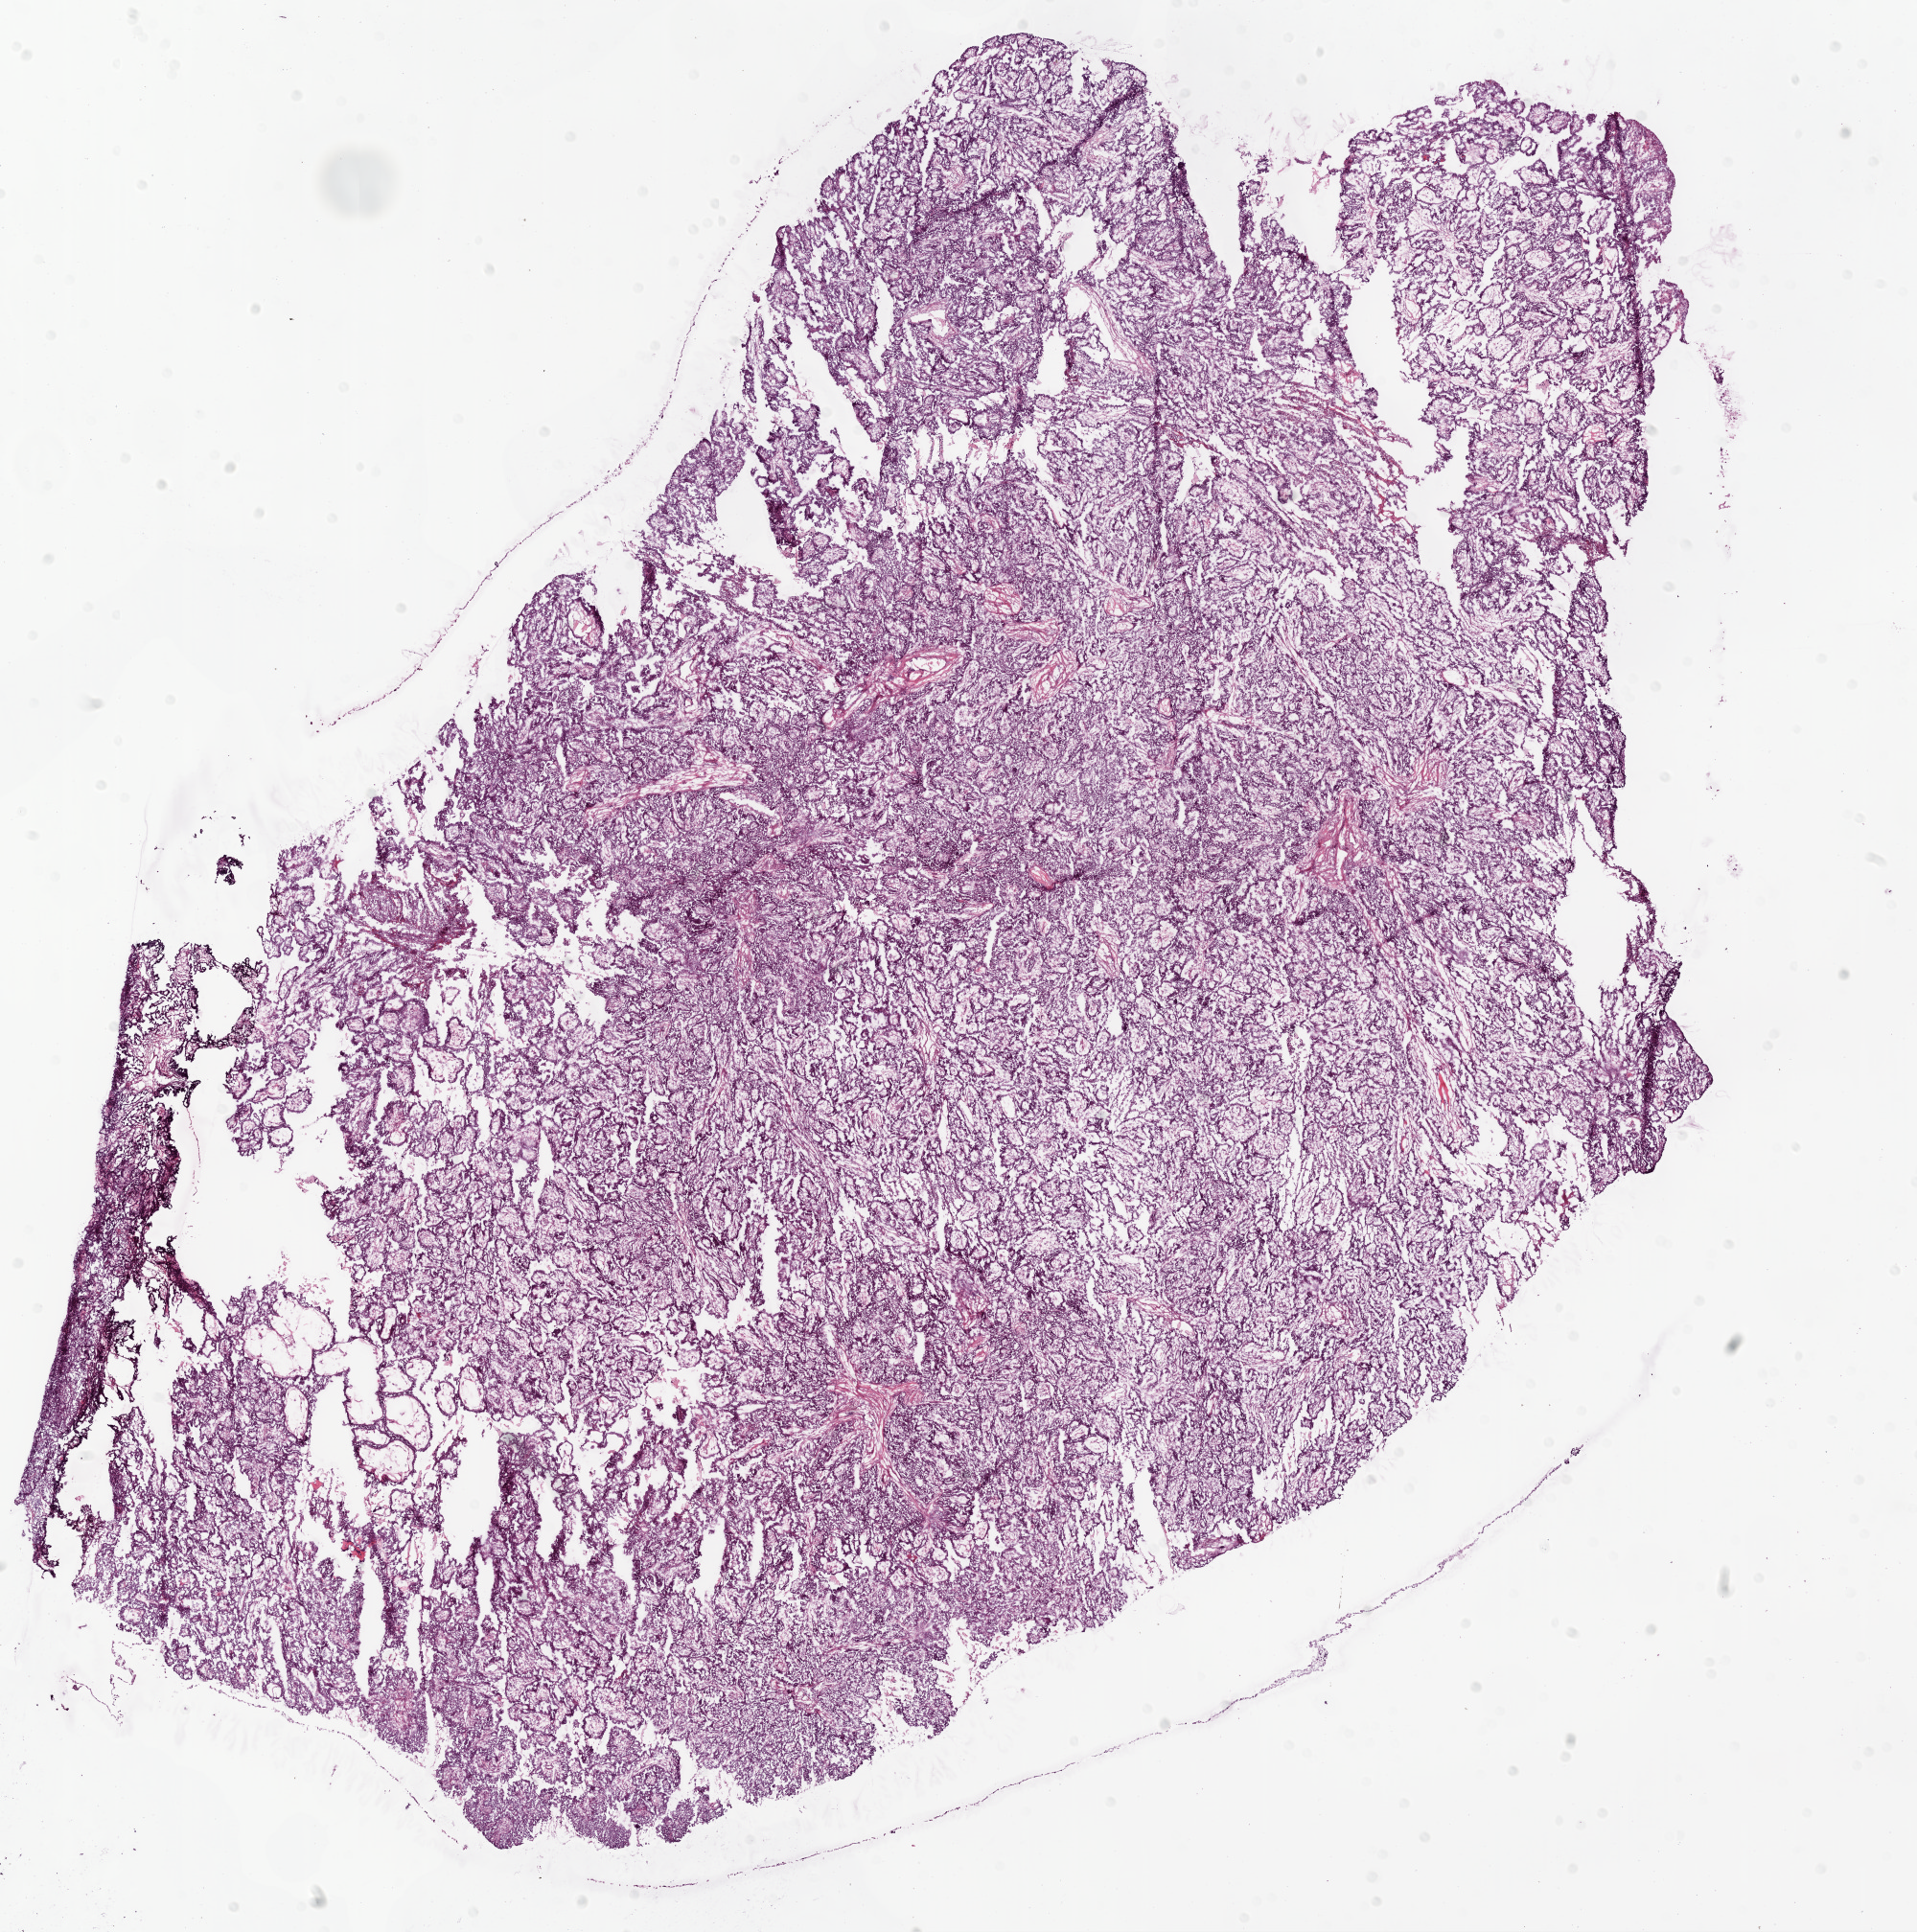
H&E whole-slide image — whole scanned area (about 16.0 x 16.2 mm, acquisition: 20x scan) shown as a low-resolution overview, frozen section from the bottom of the tissue portion, sample: primary tumour, ovary. Patient: female, age at initial diagnosis 45 years. Histologic grade: G2 (moderately differentiated). Pathologist review of this section (percent, as recorded): tumour cells 98%, tumour nuclei 90%, normal cells 0%, stromal cells 0%, necrosis 2%. Infiltration values recorded for this section: lymphocyte infiltration 2%, monocyte infiltration 3%.
Histologic diagnosis: Serous cystadenocarcinoma, NOS. FIGO stage: IIIC.